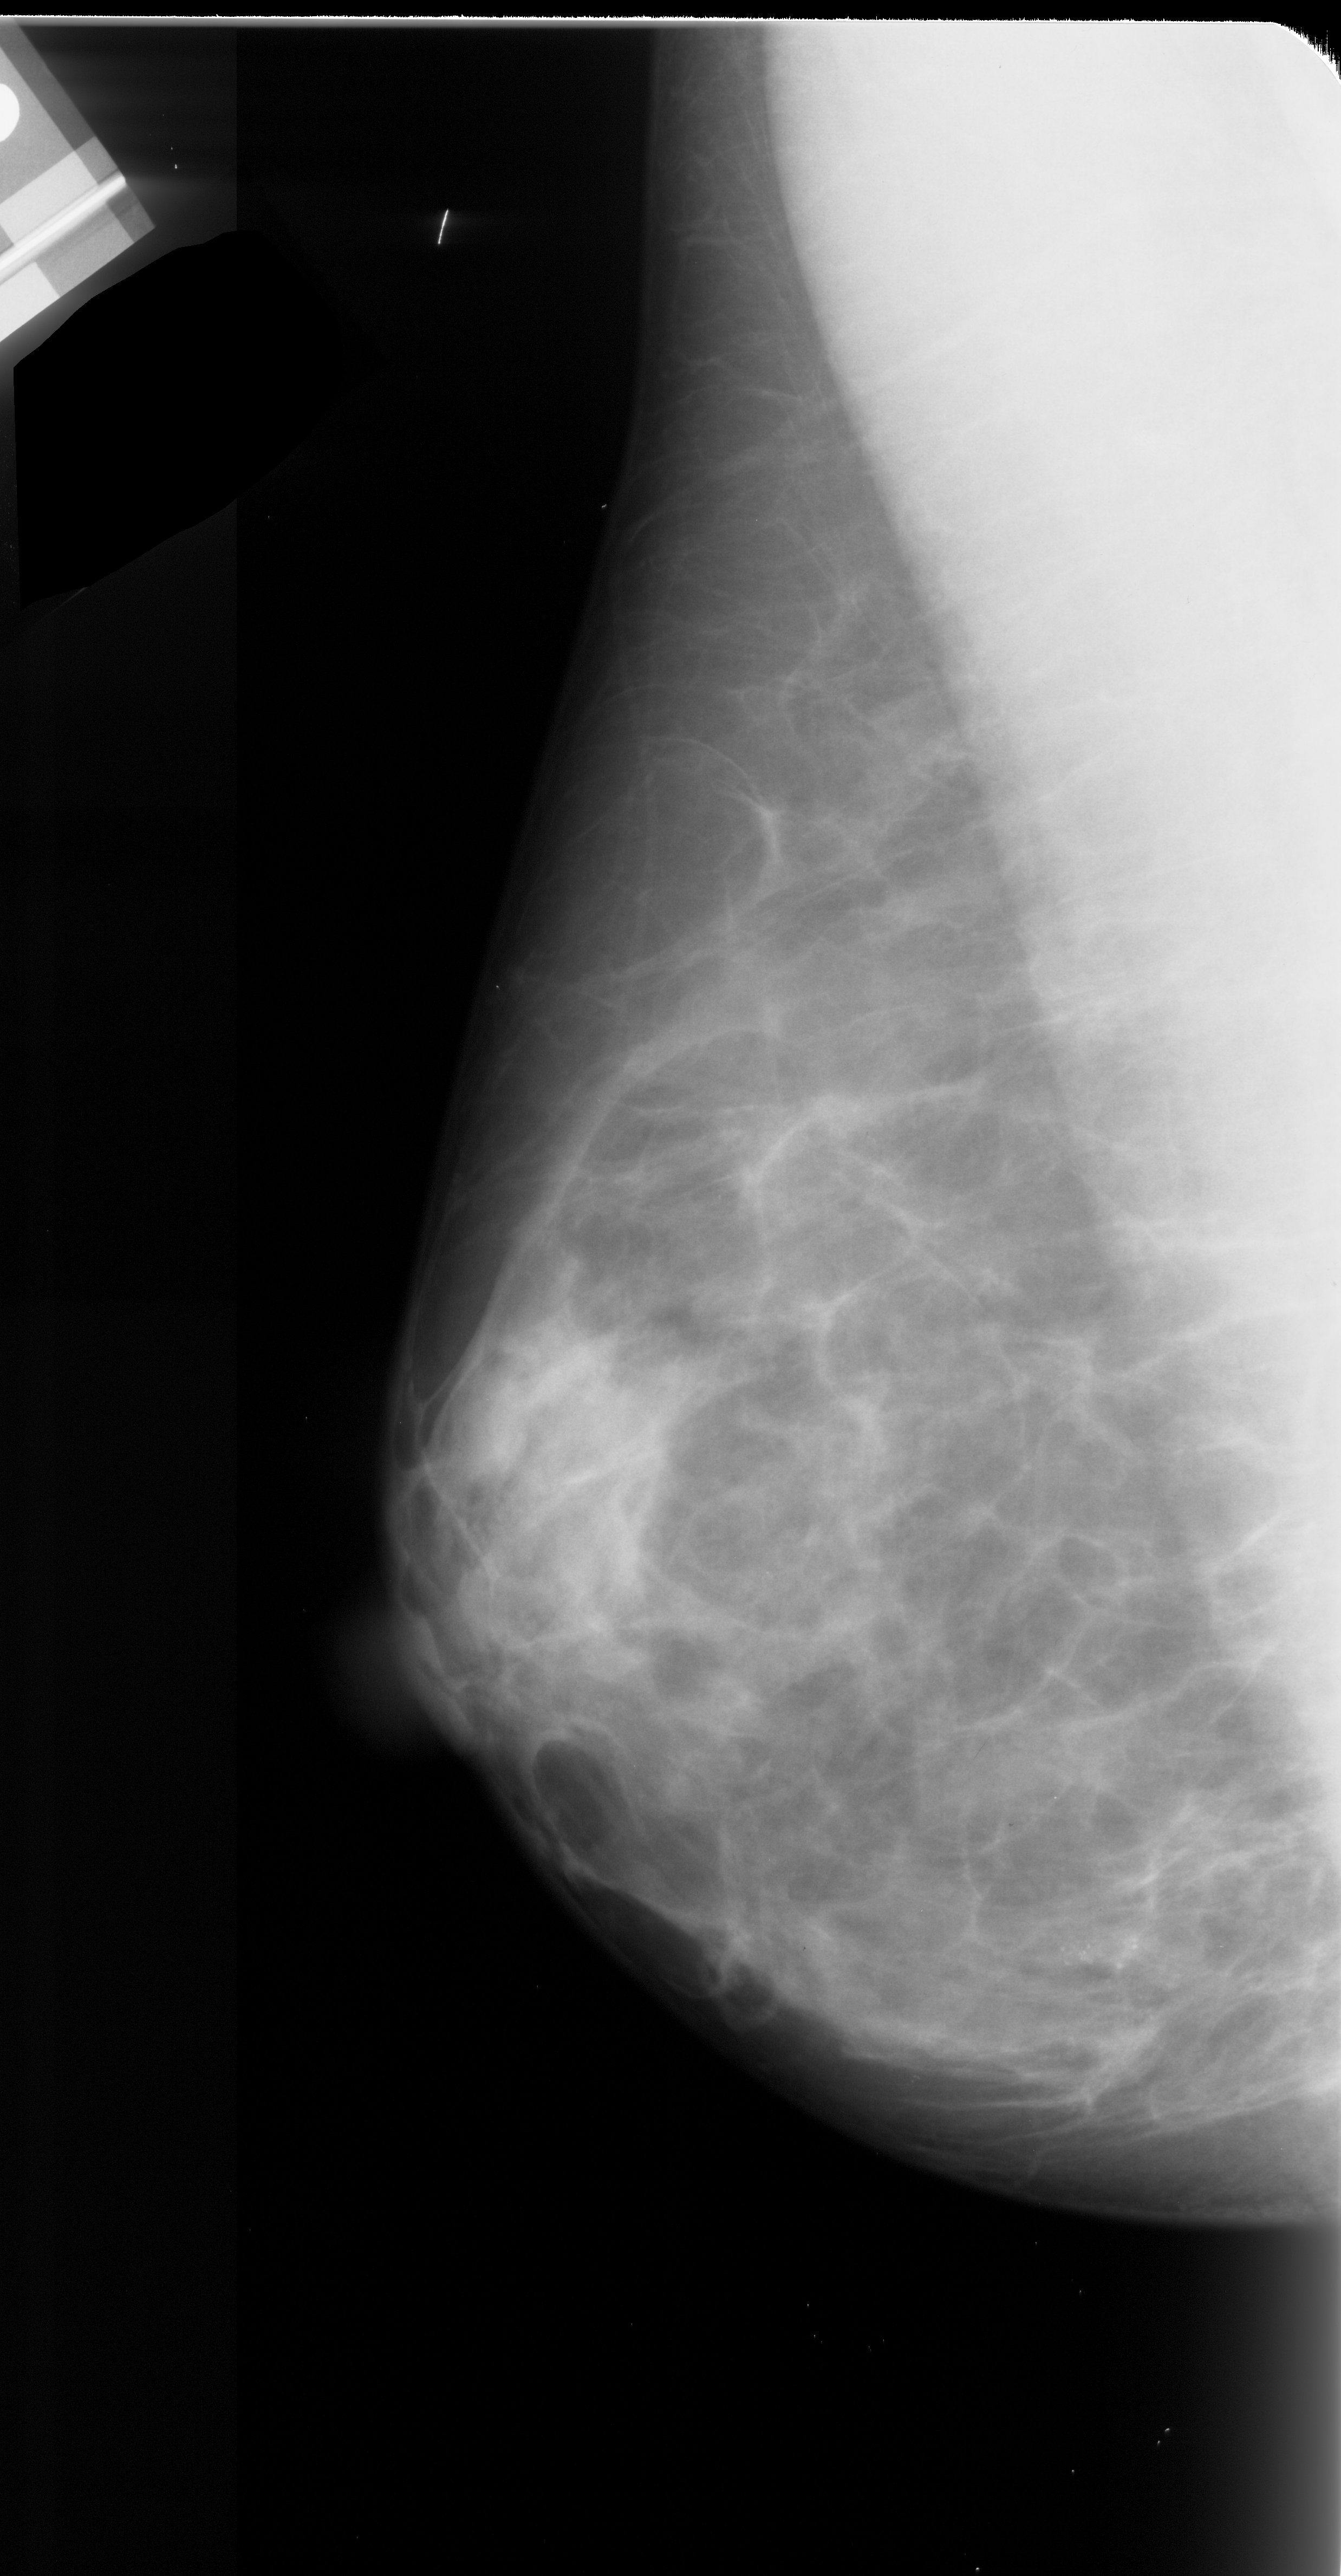
Digitized screen-film mammogram; left breast; MLO view; 1341 × 2576 image matrix.
Expert-marked regions of interest on this image (one box per marked abnormality):
- calcifications, morphology pleomorphic, distribution clustered; BI-RADS assessment category 4; subtlety rating 3 on a 1 (subtle) to 5 (obvious) scale; pathology (as recorded): malignant: box from (x=1046, y=1926) to (x=1191, y=2052) px